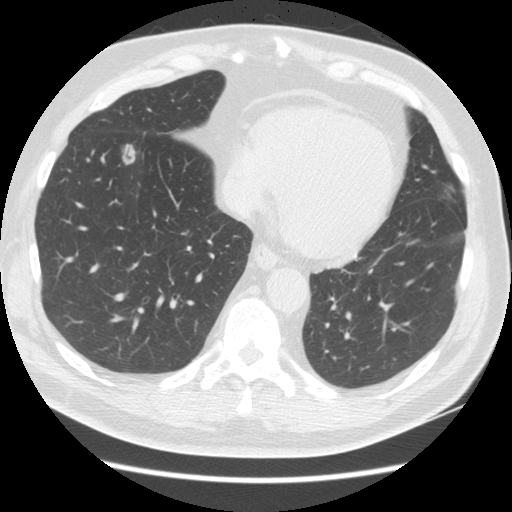
Low-dose screening chest CT, one axial slice; position 51 of 161 along the scan axis; 140 kVp; lung window (W 1500 / L -600 HU); 512 × 512 image matrix.
Structures marked on this image (manually delineated by an expert):
- lesion 1 (tumor, lower lobe of right lung): bounding box (x1, y1, x2, y2) in pixels: (122, 144, 136, 165)